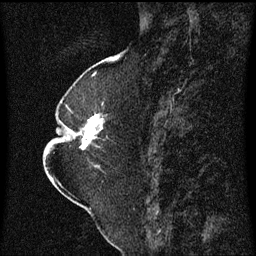
Breast MRI (dynamic contrast-enhanced), one sagittal slice; slice 26 of 60 in the series (ordered by position); dynamic contrast-enhanced series, image 2 of 3 at this slice position (ordered by acquisition); 1.5 T; TE 4.2 ms, TR 8.4 ms; 2 mm slice thickness; 256 × 256 image matrix, field of view 200 × 200 mm. Patient: female, 52 years. From the clinical record (not read from this slice): setting: breast cancer imaged before/during neoadjuvant chemotherapy; receptor status: HR-positive, HER2-negative.
Outlined on this slice (semi-automatic segmentation, software-assisted and operator-edited):
- analysis volume of interest (the breast-tissue region the enhancement analysis was run in; not a lesion): box from (x=64, y=108) to (x=109, y=167) px
- tumour enhancement mask (voxels above the 70 % enhancement threshold inside the analysis volume of interest): (x=82, y=114)–(x=104, y=149)